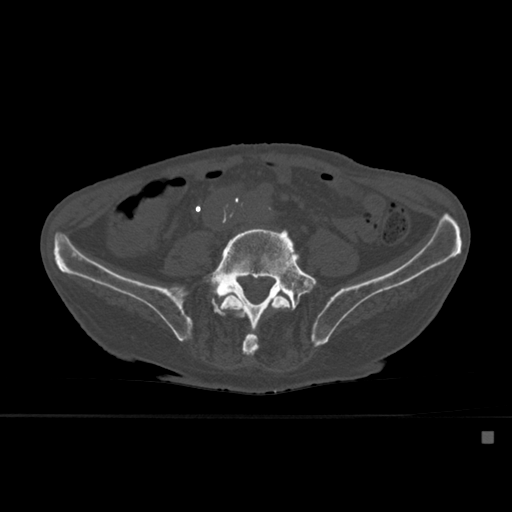
CT including the spine, one axial slice; position 180 of 527 along the scan axis; bone window (W 1800 / L 400 HU); 512 × 512 image matrix, field of view 373 × 373 mm. Patient: male, 78 years. Case-level facts recorded for this patient, not image findings: primary cancer: prostate.
Outlined on this slice (semi-automatically segmented with operator editing):
- L4 vertebra: bounding box (x1, y1, x2, y2) in pixels: (220, 292, 294, 356)
- L5 vertebra: (204, 227, 317, 343)